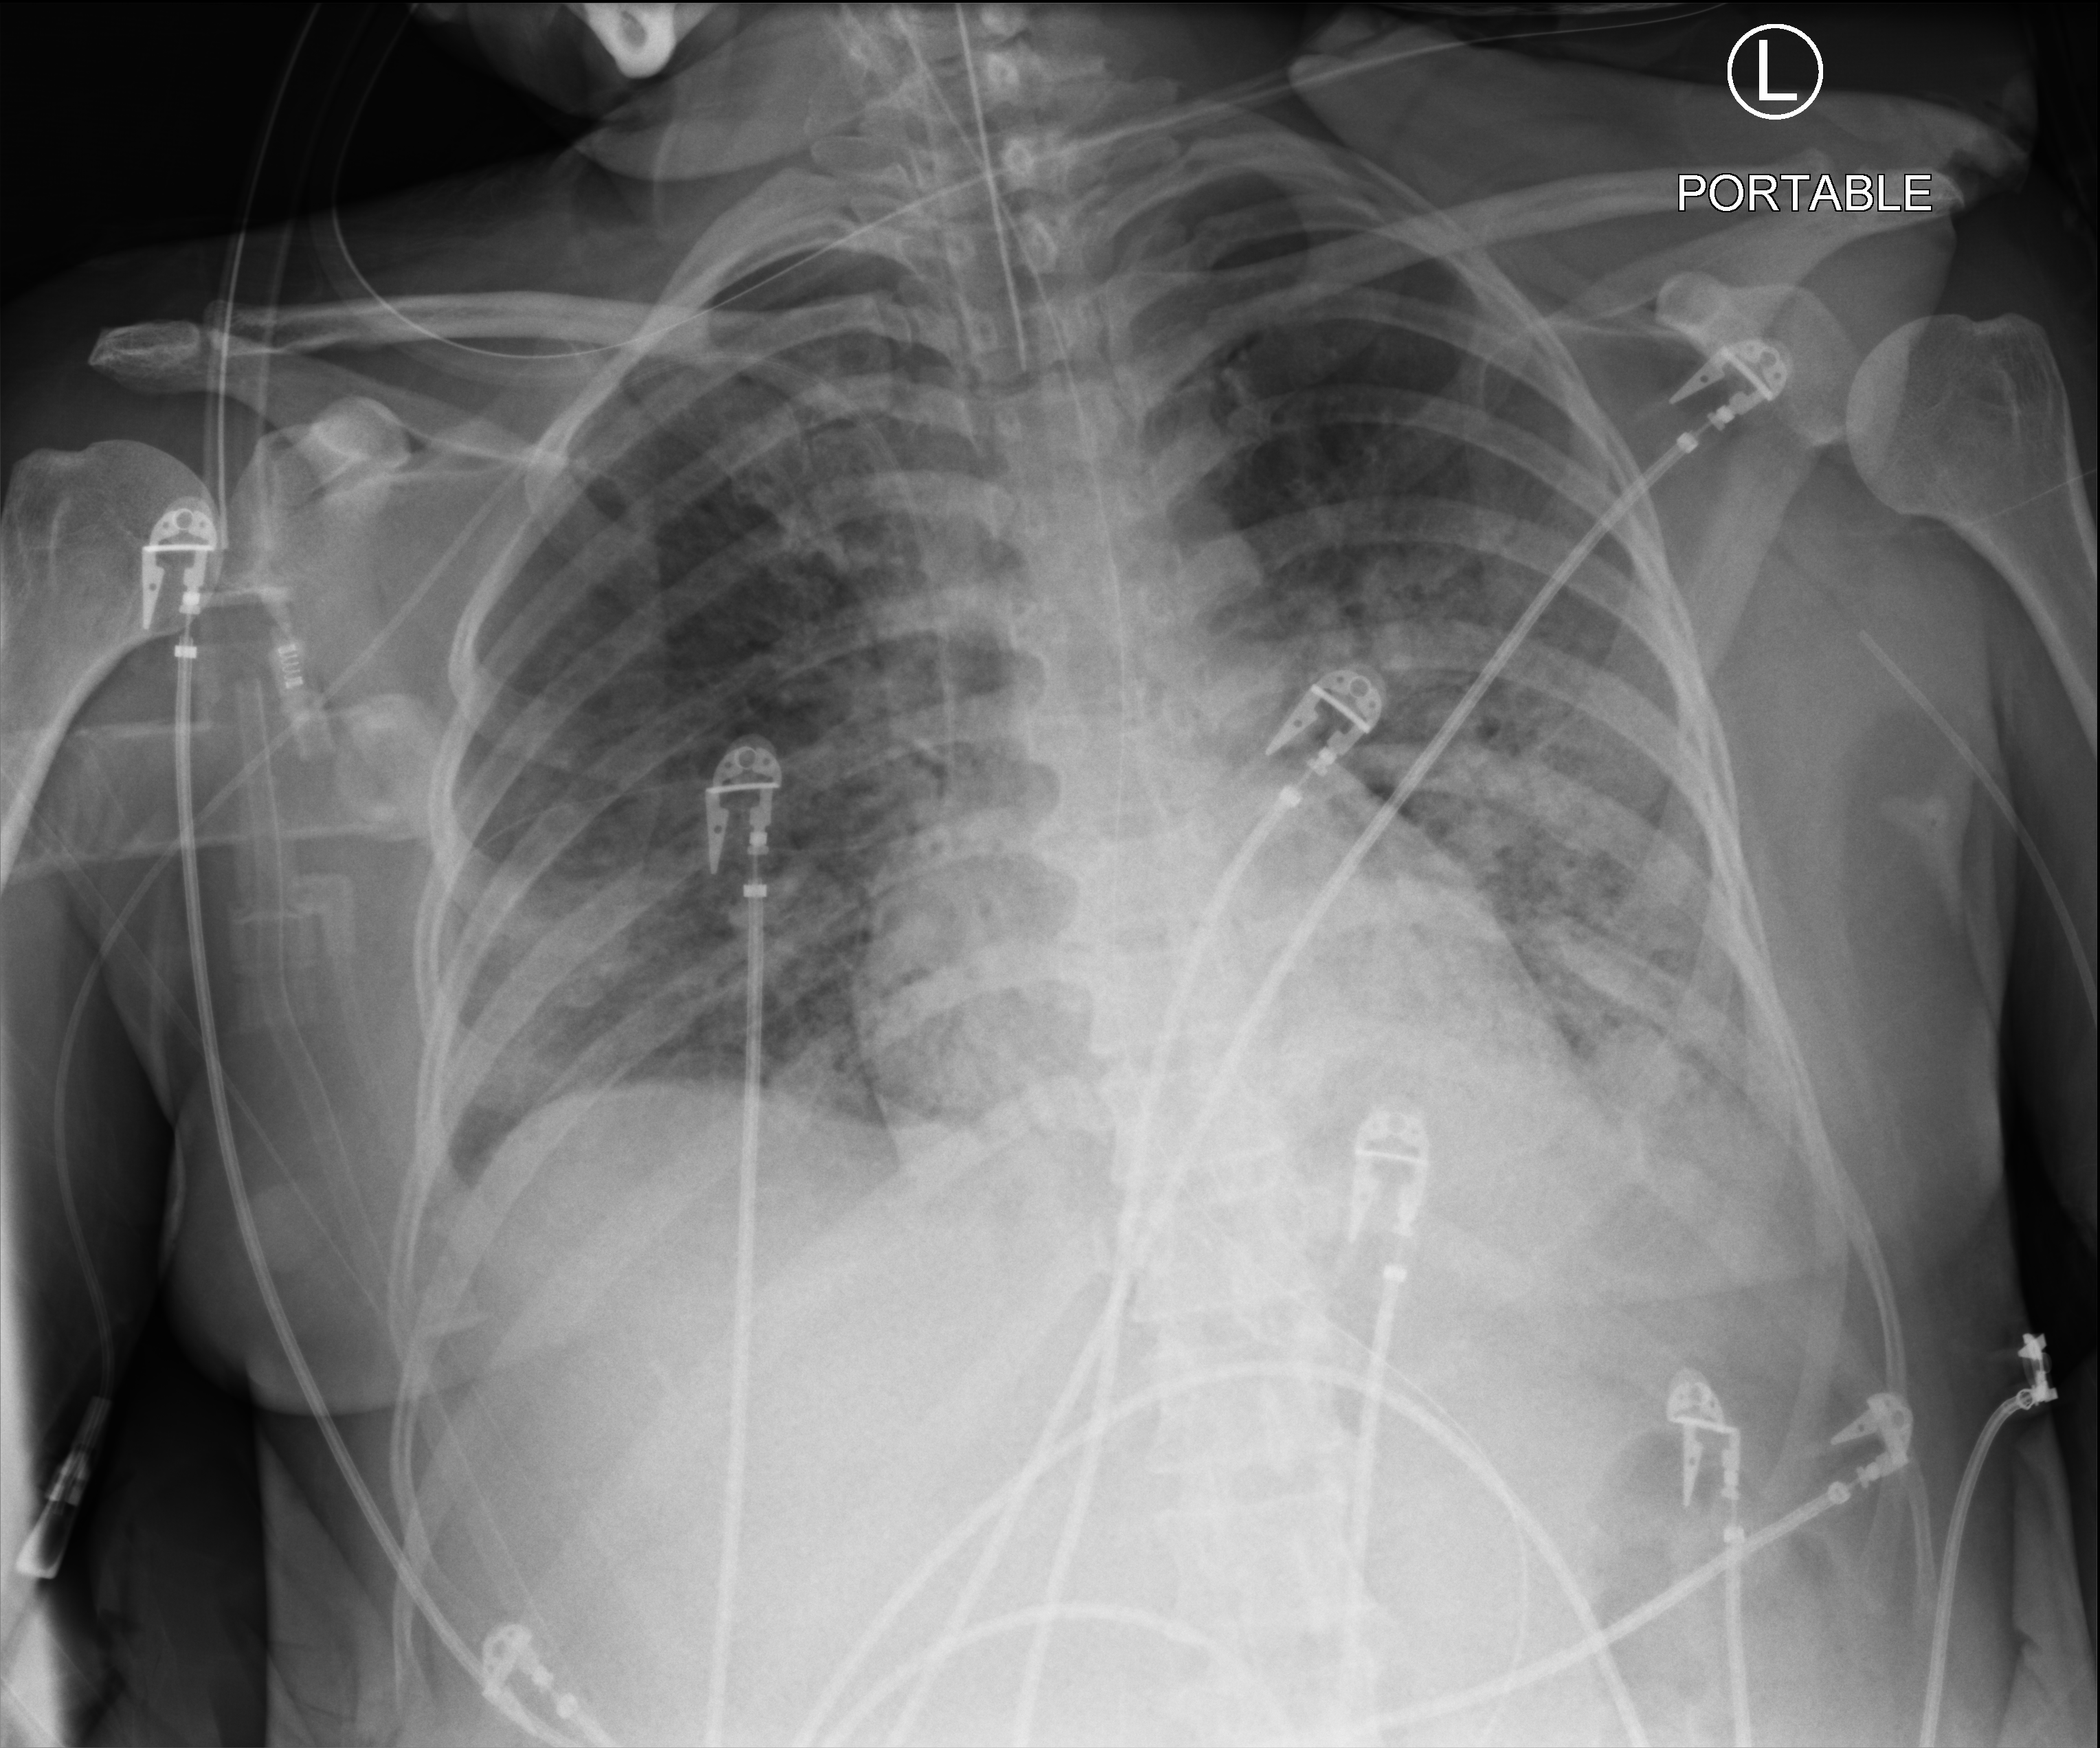
Bedside chest radiograph (computed radiography); anteroposterior (AP) projection. Female patient hospitalised with COVID-19, age 18–59 years.
Admission-level facts for this patient (not findings on this image; timing relative to this image not recorded): admitted to intensive care during this hospital stay: yes; mechanically ventilated during this hospital stay: yes.